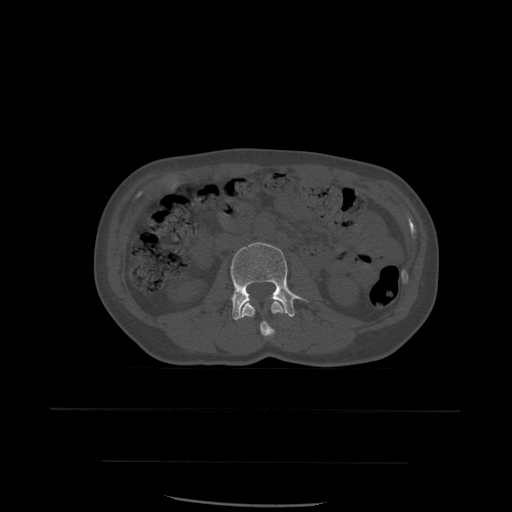
CT including the spine, one axial slice. Position 206 of 574 along the scan axis. Bone window (W 1800 / L 400 HU). 1.25 mm slice thickness. 512 × 512 image matrix. Patient age 48 years. From the clinical record (not read from this slice): primary cancer: lung; vertebrae with lytic lesions (as recorded): T11.
Annotated regions visible in this slice (semi-automatically segmented with operator editing):
- L2 vertebra: bounding box (x1, y1, x2, y2) in pixels: (240, 301, 284, 337)
- L3 vertebra: (231, 242, 307, 320)